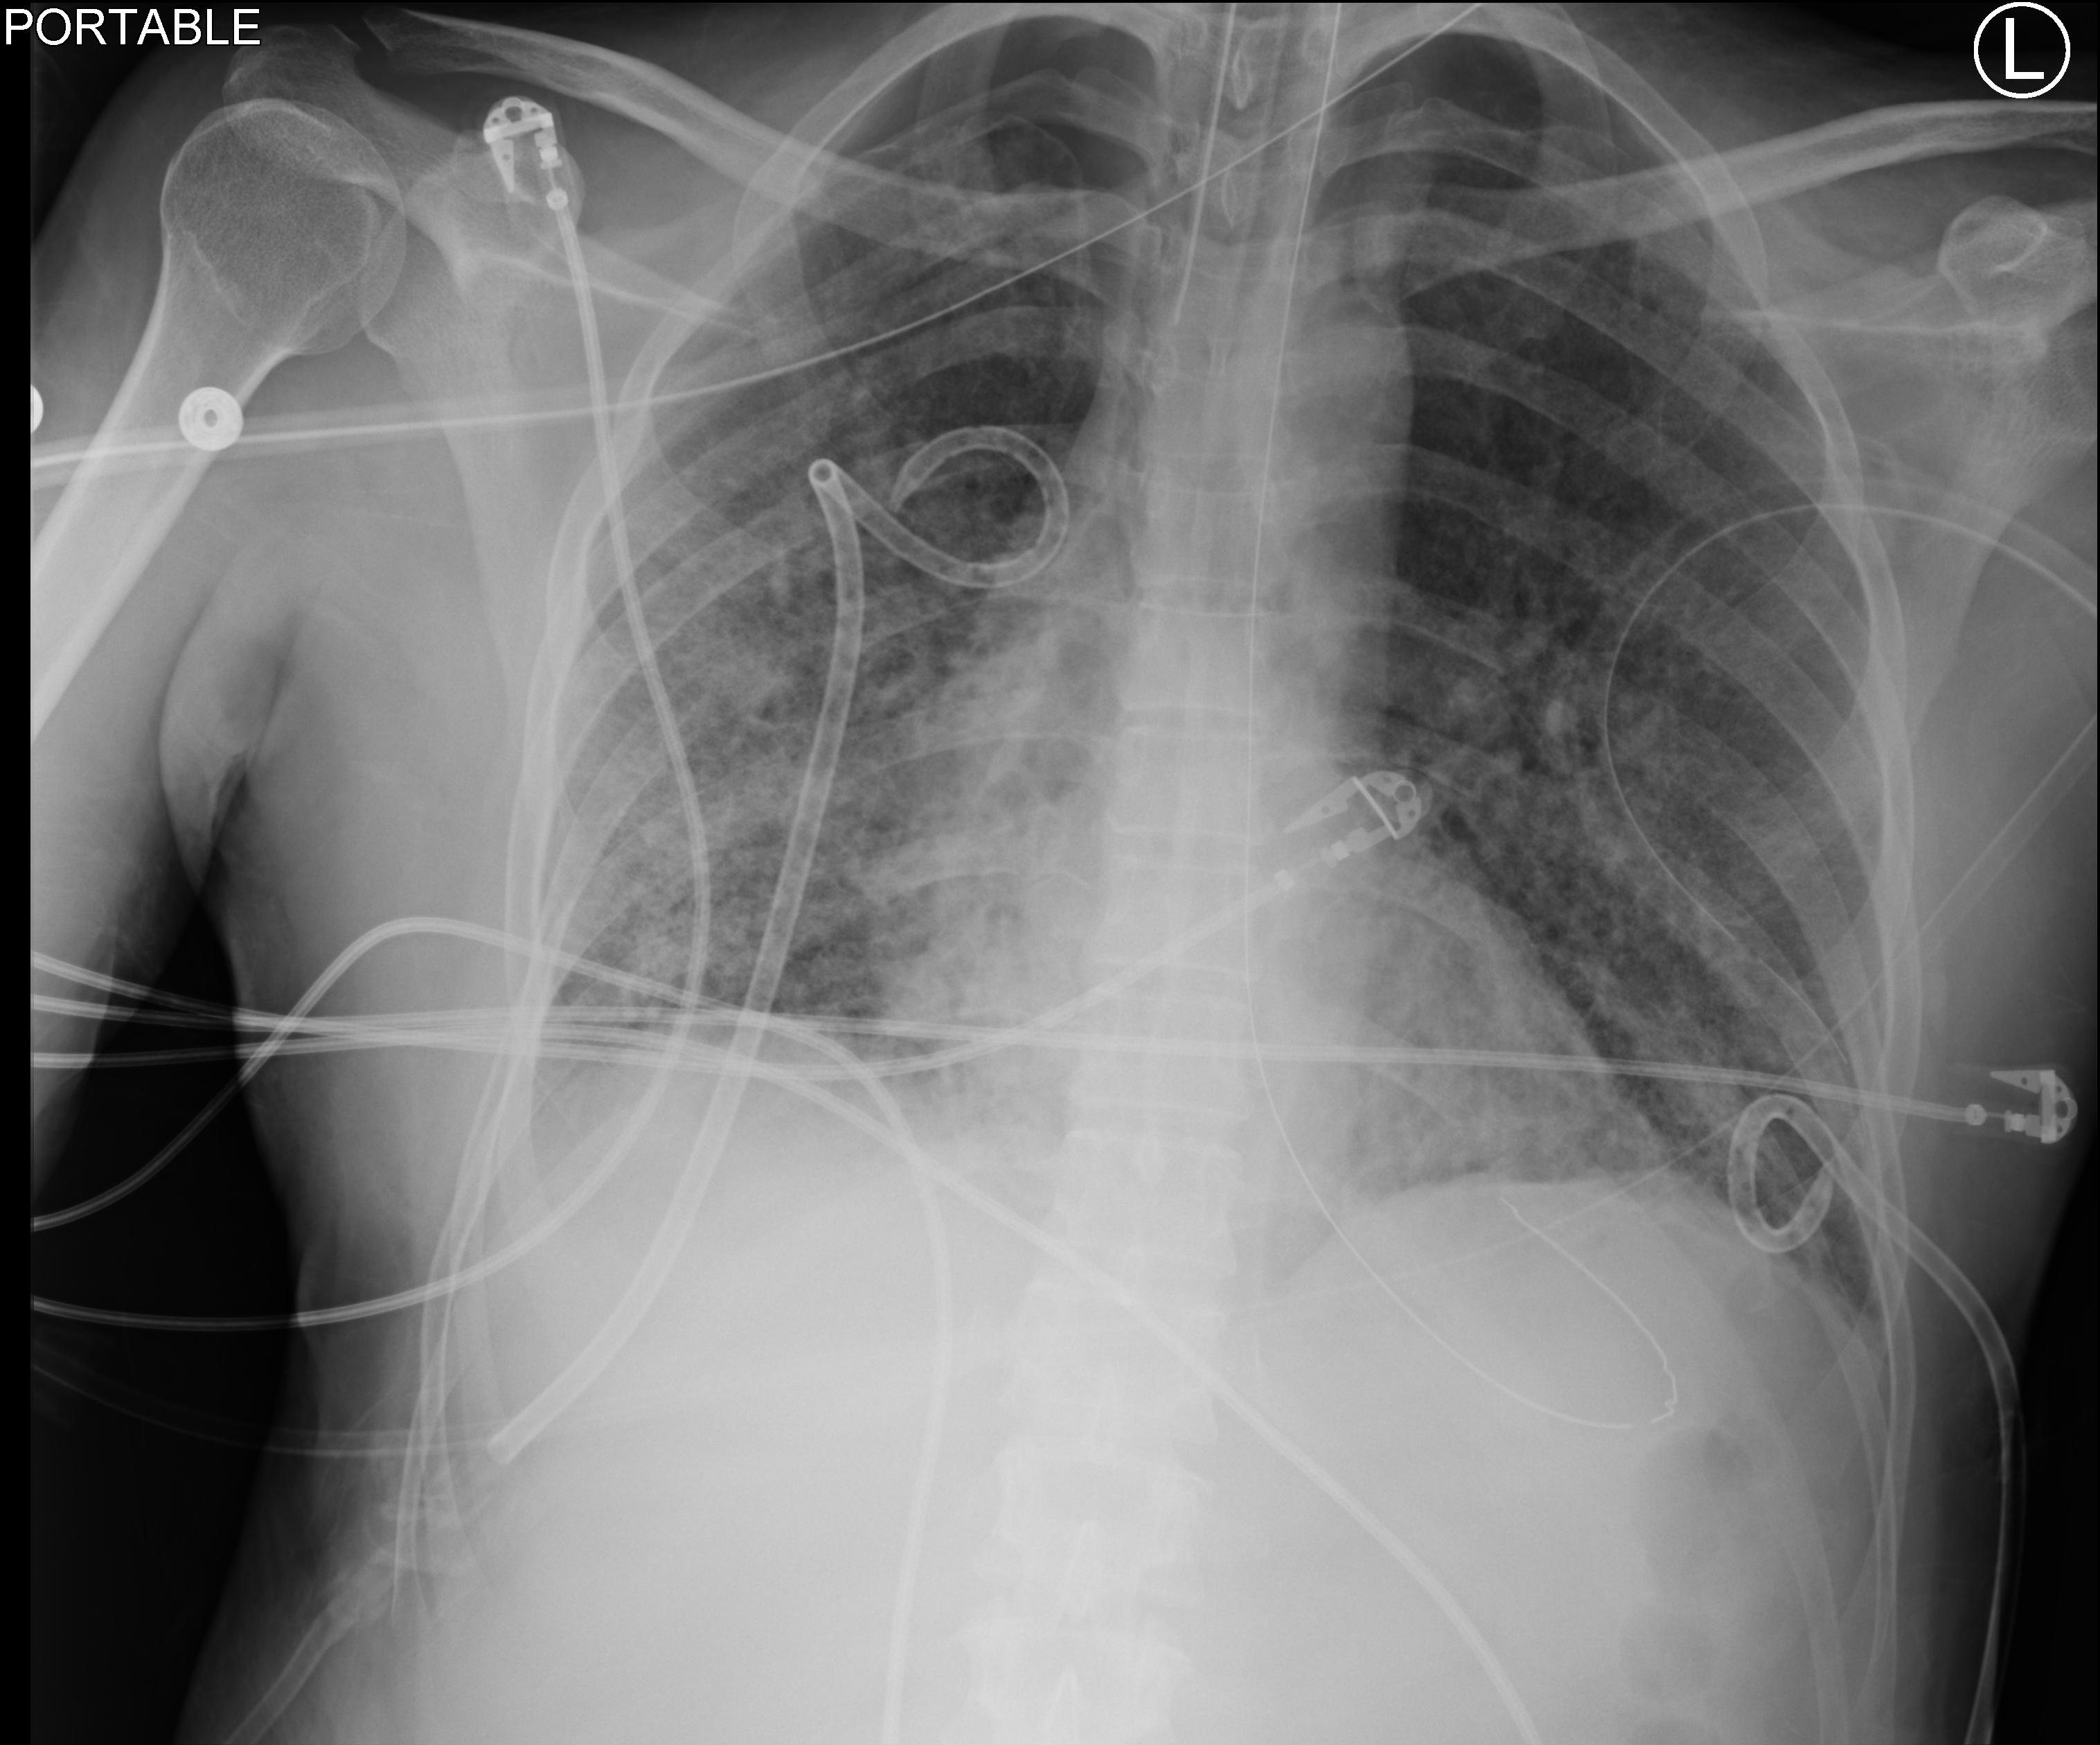
Portable chest radiograph, anteroposterior (AP) projection. Adult patient hospitalised with COVID-19, age 18–59 years.
Hospital-stay facts (about this admission, not read from this image; timing relative to this image not recorded): smoking status (admission record): never; mechanically ventilated during this hospital stay: yes.